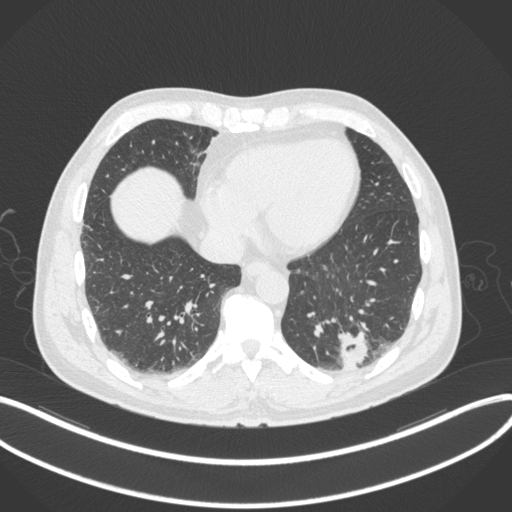
Chest CT, one axial slice; slice 83 of 313 in the series (ordered by position); reconstruction kernel B31f; 120 kVp; lung window (W 1500 / L -600 HU); 512 × 512 image matrix. Patient: male, 54 years. From the clinical record (not read from this slice): clinical TNM (as recorded): T1c N0 M1; histopathological grade: G3.
Outlined on this slice (bounding box drawn by a radiologist):
- lung tumour (recorded histology: adenocarcinoma): bounding box (x1, y1, x2, y2) in pixels: (334, 320, 373, 375)